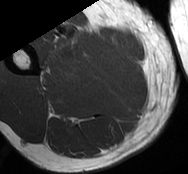
MRI of an extremity soft-tissue mass, one axial slice. Slice 21 of 93 in the series (ordered by position). MR volume resampled by the dataset authors to the PET/CT grid (not the native acquisition matrix). 188 × 174 image matrix, field of view 184 × 170 mm. Male patient. From the clinical record (not read from this slice): histological type: undifferentiated - pleiomorphic; grade: high; site of the primary tumour: right thigh.
Annotated regions visible in this slice (expert contour drawn on MRI and transferred to this co-registered scan by the dataset authors):
- gross tumour volume including surrounding oedema: bounding box <52,37,119,70> (left, top, right, bottom; pixels)